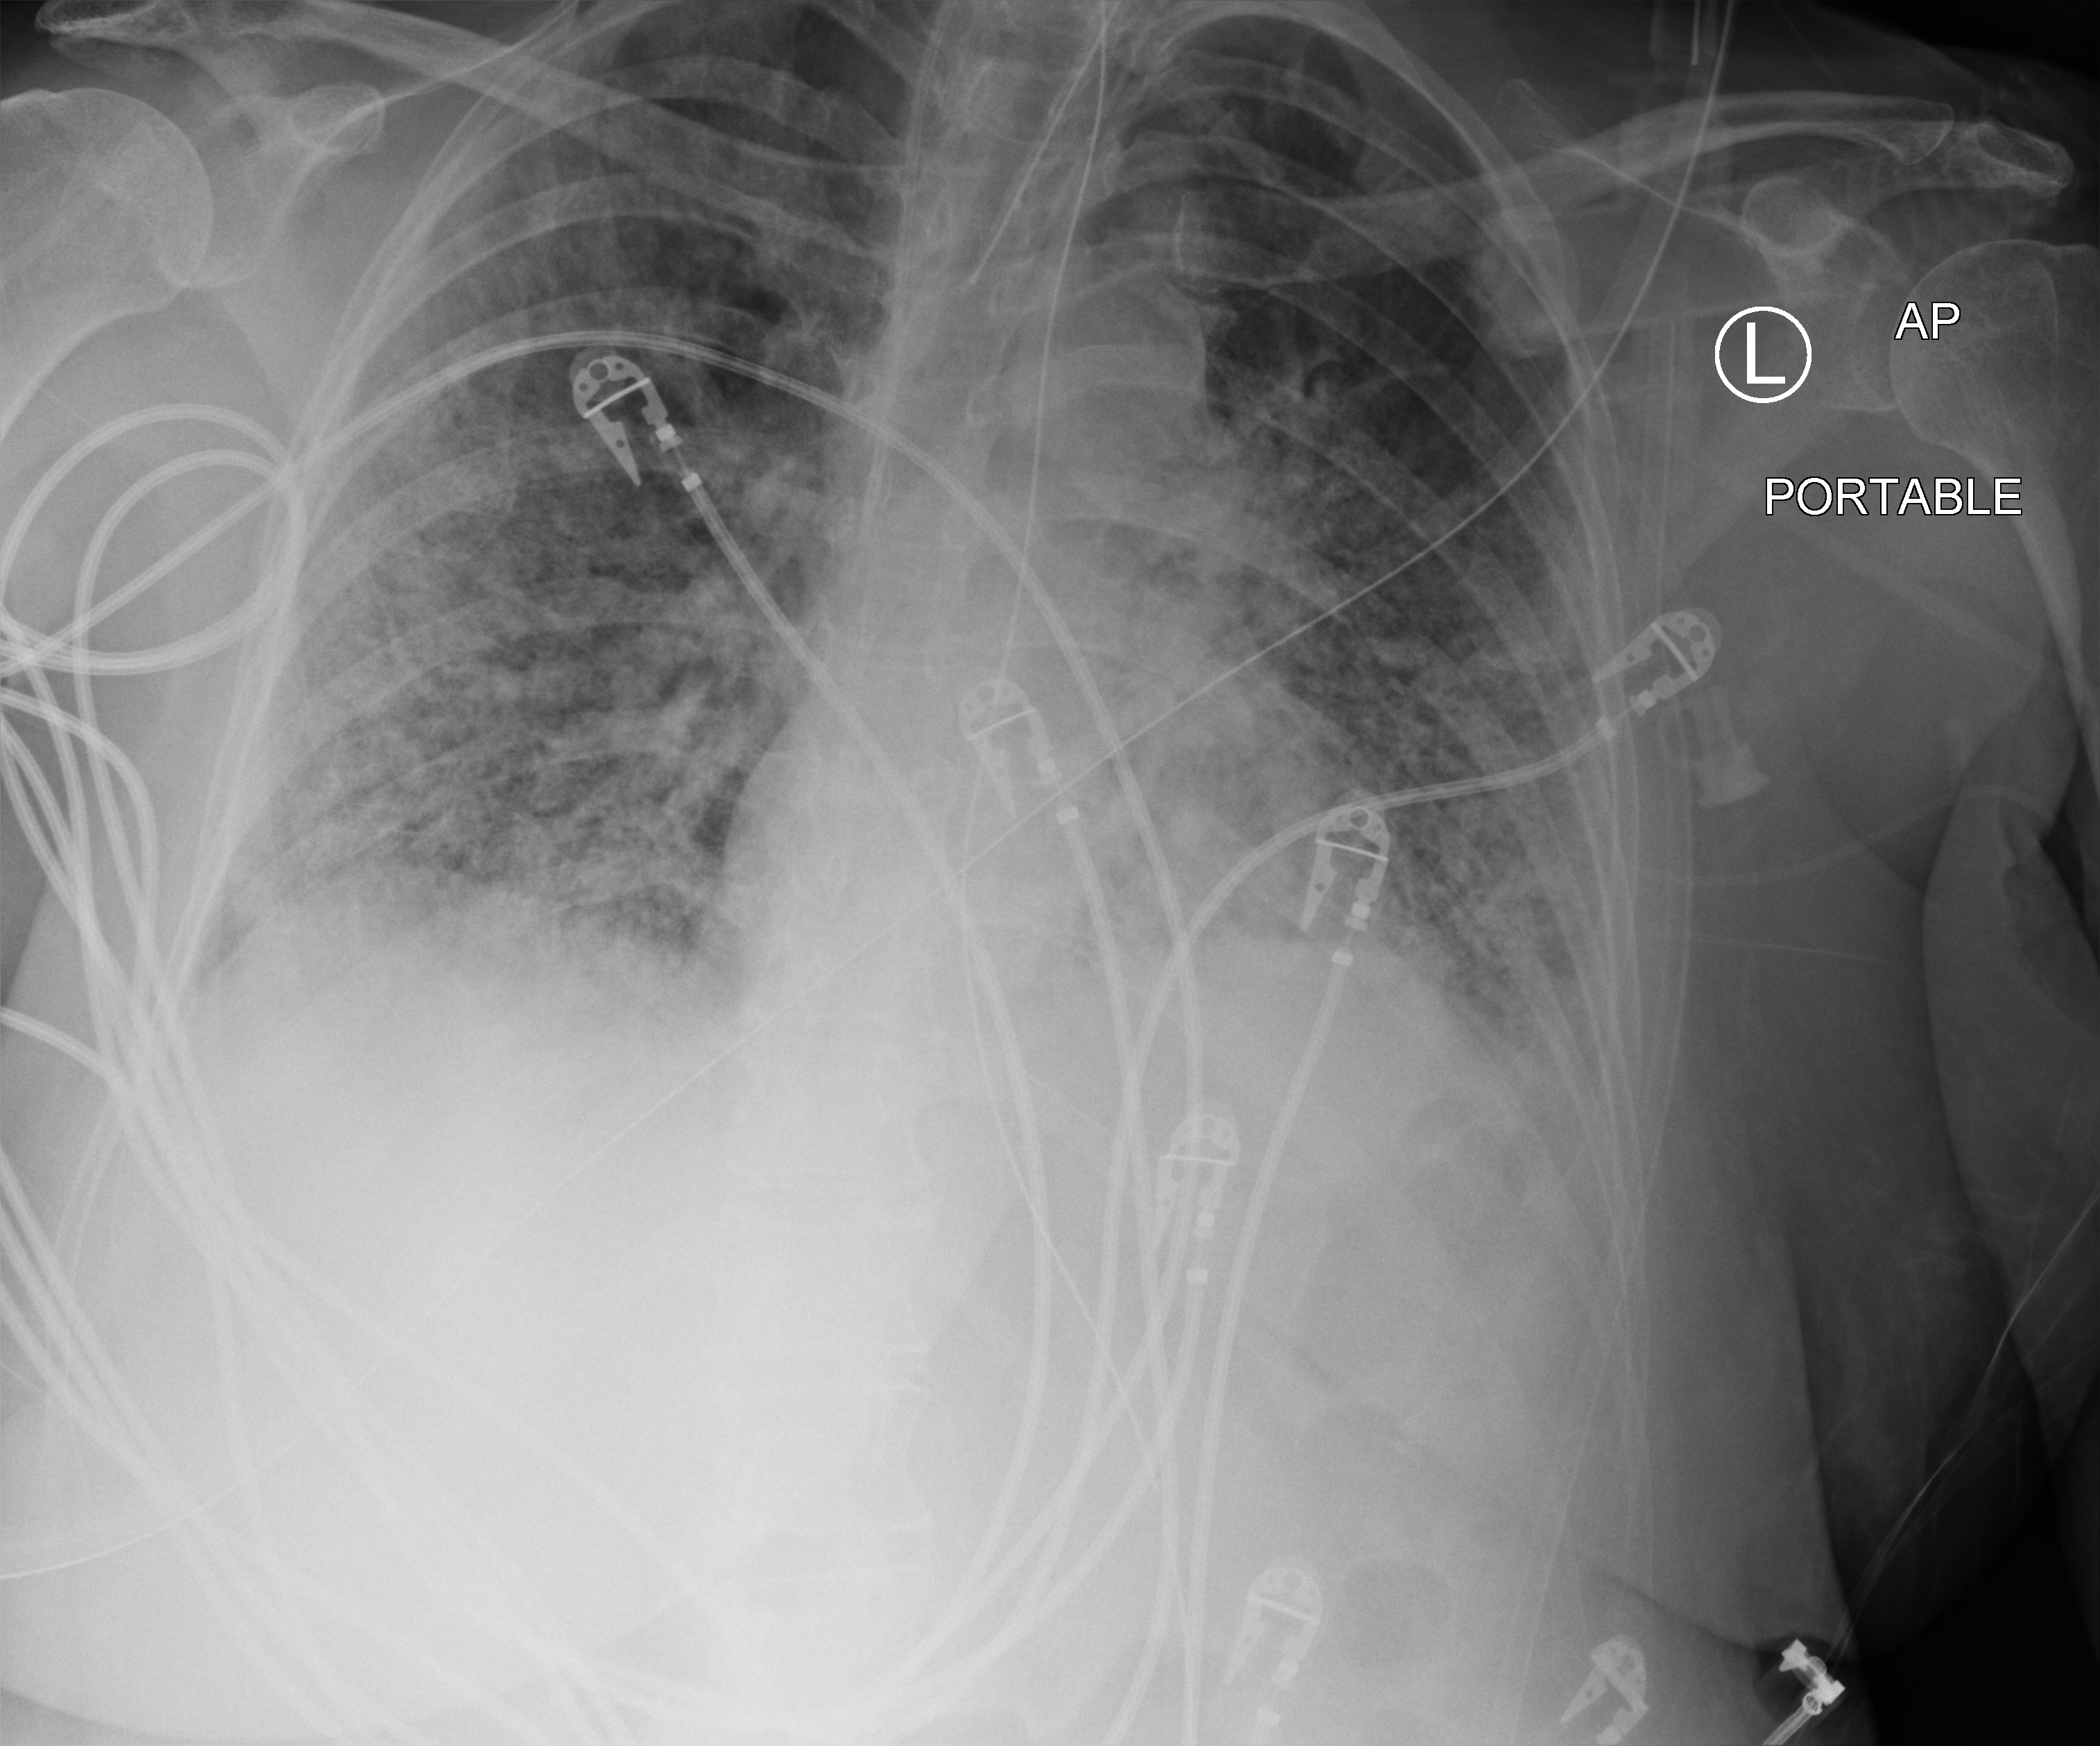
Bedside chest radiograph (computed radiography), anteroposterior (AP) projection. Female patient hospitalised with COVID-19, age 60–74 years.
From the hospital-stay record, not from the radiograph (when in the stay this image was taken is not recorded):
- diabetes (admission record): no